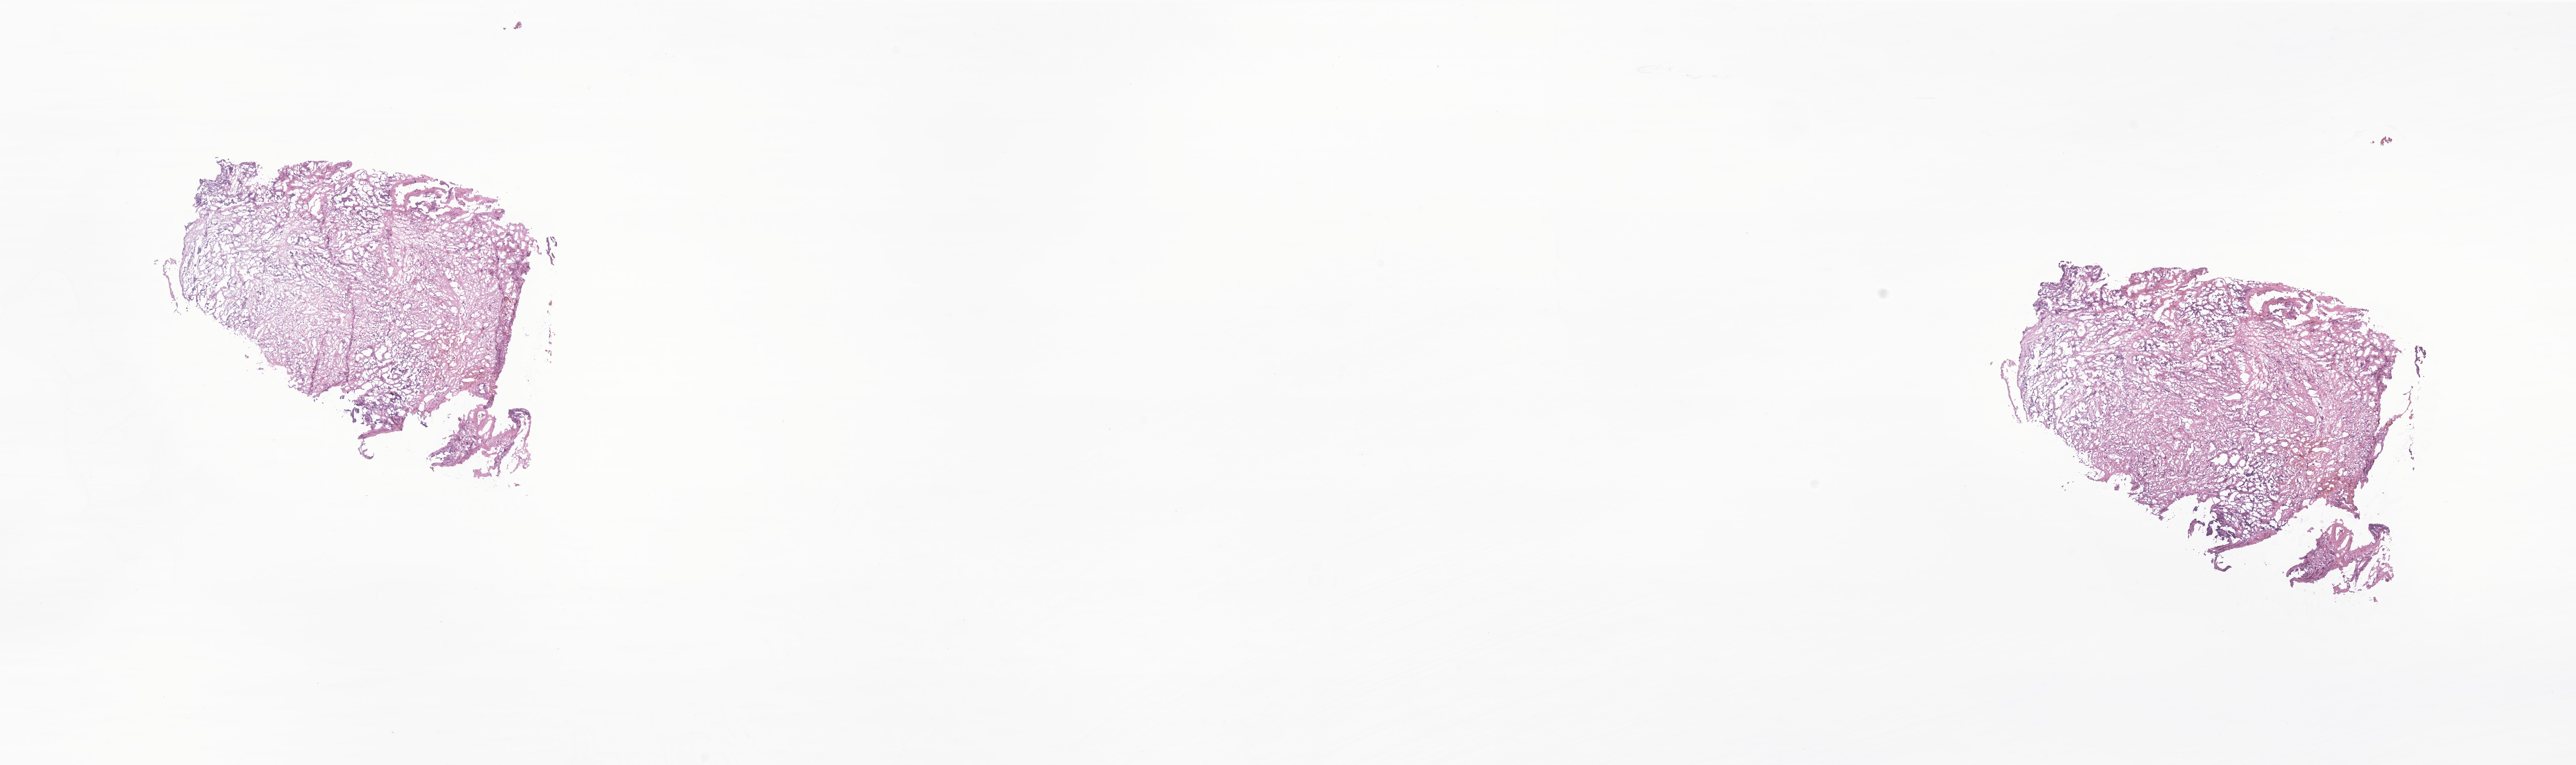
Whole-slide image, H&E stain of tumor tissue from the spinal cord — a low-resolution overview of the entire scanned area, about 29.7 x 8.8 mm; frozen section (OCT-embedded). Male patient, age 210 months (17 years 6 months).
Diagnosis (ICD-O-3 morphology term): Alveolar rhabdomyosarcoma.